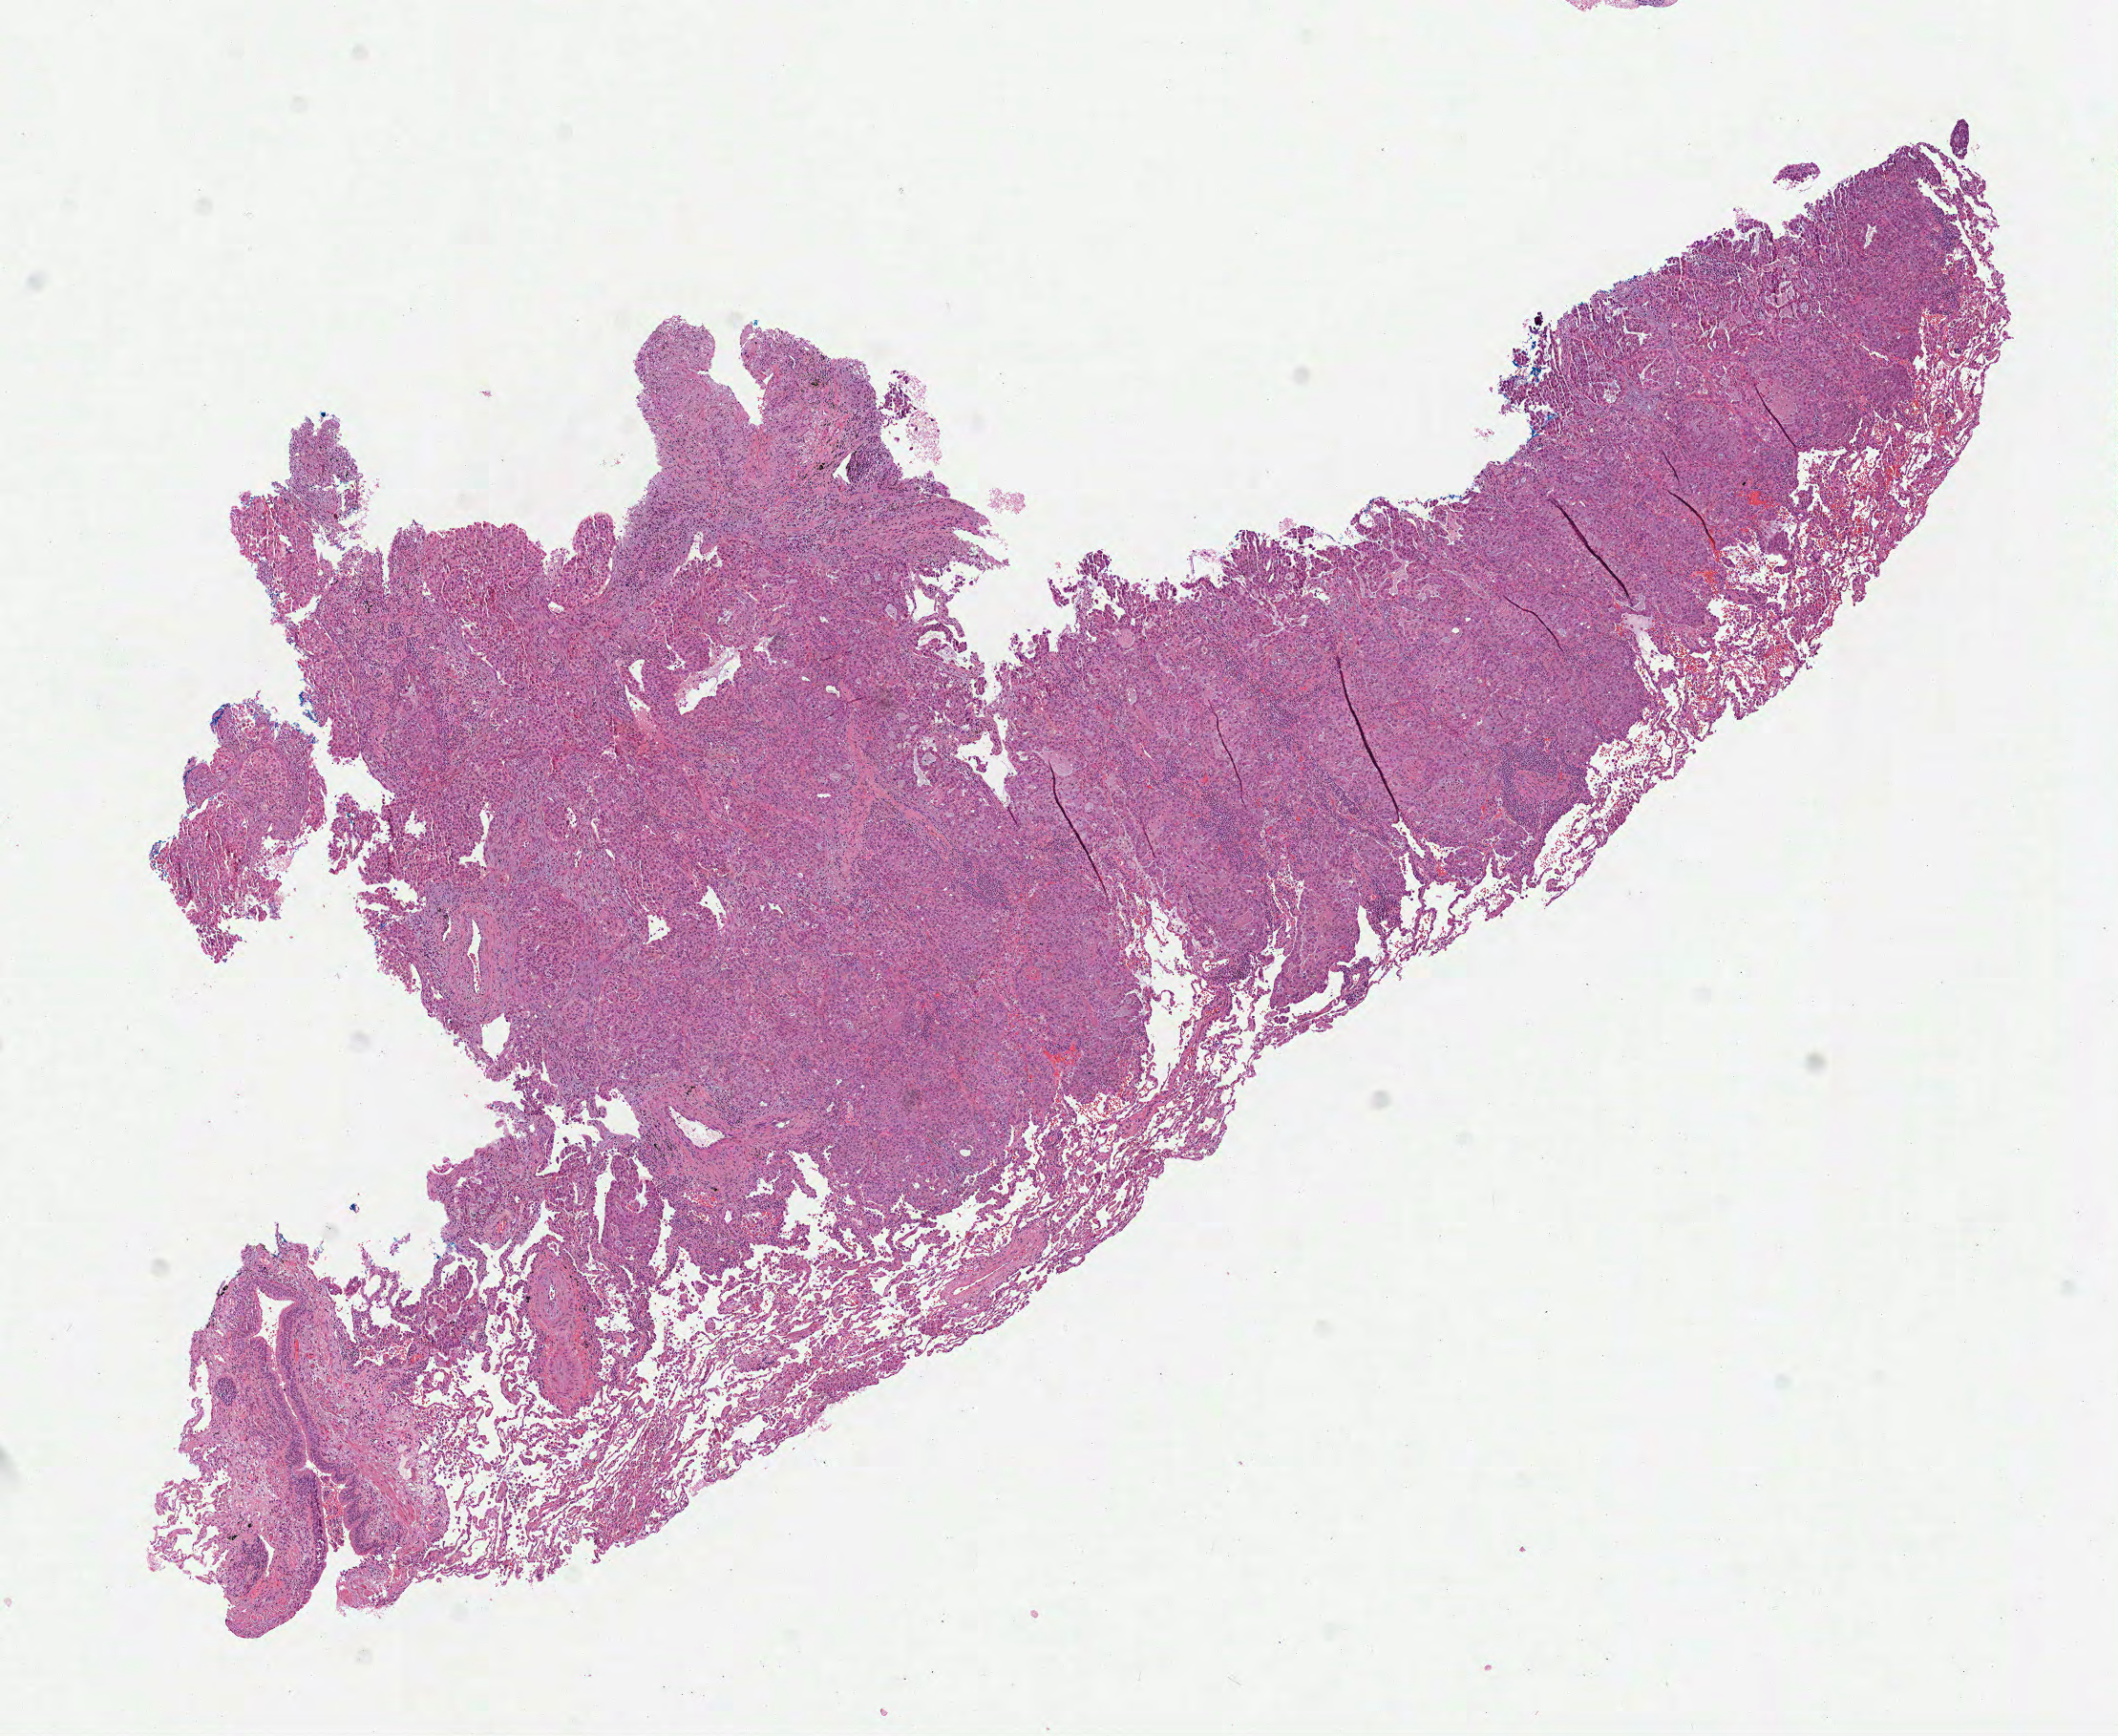
H&E whole-slide image — a low-resolution overview of the entire scanned area, about 8.9 x 7.3 mm (from a 40x scan). Formalin-fixed paraffin-embedded (FFPE) diagnostic section. Lung, primary tumour sample. Male, age 80 years at initial diagnosis.
Pathologic diagnosis: Adenocarcinoma, NOS (lower lobe, lung). TNM: T1a N0 M0. AJCC pathologic stage: IA.